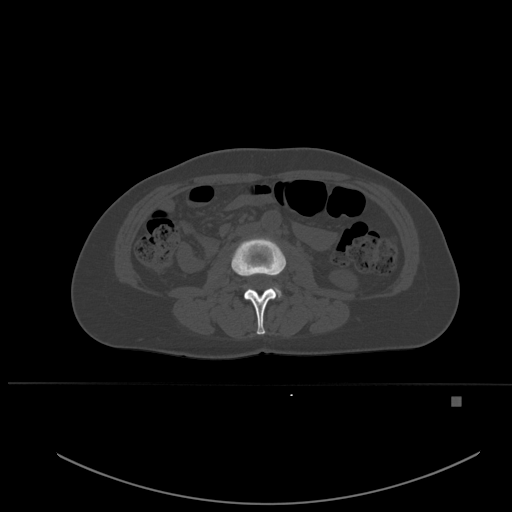
CT including the spine, one axial slice; bone window (W 1800 / L 400 HU); 1.5 mm slice thickness; 512 × 512 image matrix, field of view 443 × 443 mm. Patient: female, 49 years. Case-level facts recorded for this patient, not image findings: primary cancer: breast; vertebrae with lytic lesions (as recorded): L3, T12, L4.
Structures marked on this image (semi-automatic segmentation, software-assisted and operator-edited):
- L2 vertebra: bounding box (x1, y1, x2, y2) in pixels: (231, 238, 286, 335)
- L3 vertebra: (274, 286, 282, 298)